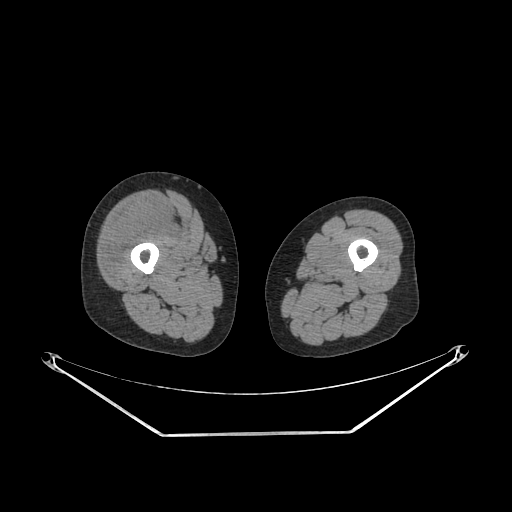
CT of an extremity soft-tissue mass (from a PET/CT study), one axial slice. Reconstruction kernel SOFT. Soft-tissue window (W 400 / L 40 HU). 3.75 mm slice thickness. 512 × 512 image matrix, field of view 500 × 500 mm. Female patient. From the clinical record (not read from this slice): histological type: pleiomorphic undifferentiated sarcoma; grade: high; site of the primary tumour: right quadricep.
Structures marked on this image (expert contour drawn on MRI and transferred to this co-registered scan by the dataset authors):
- tumour plus oedema (research contour): bounding box (x1, y1, x2, y2) in pixels: (105, 203, 177, 277)